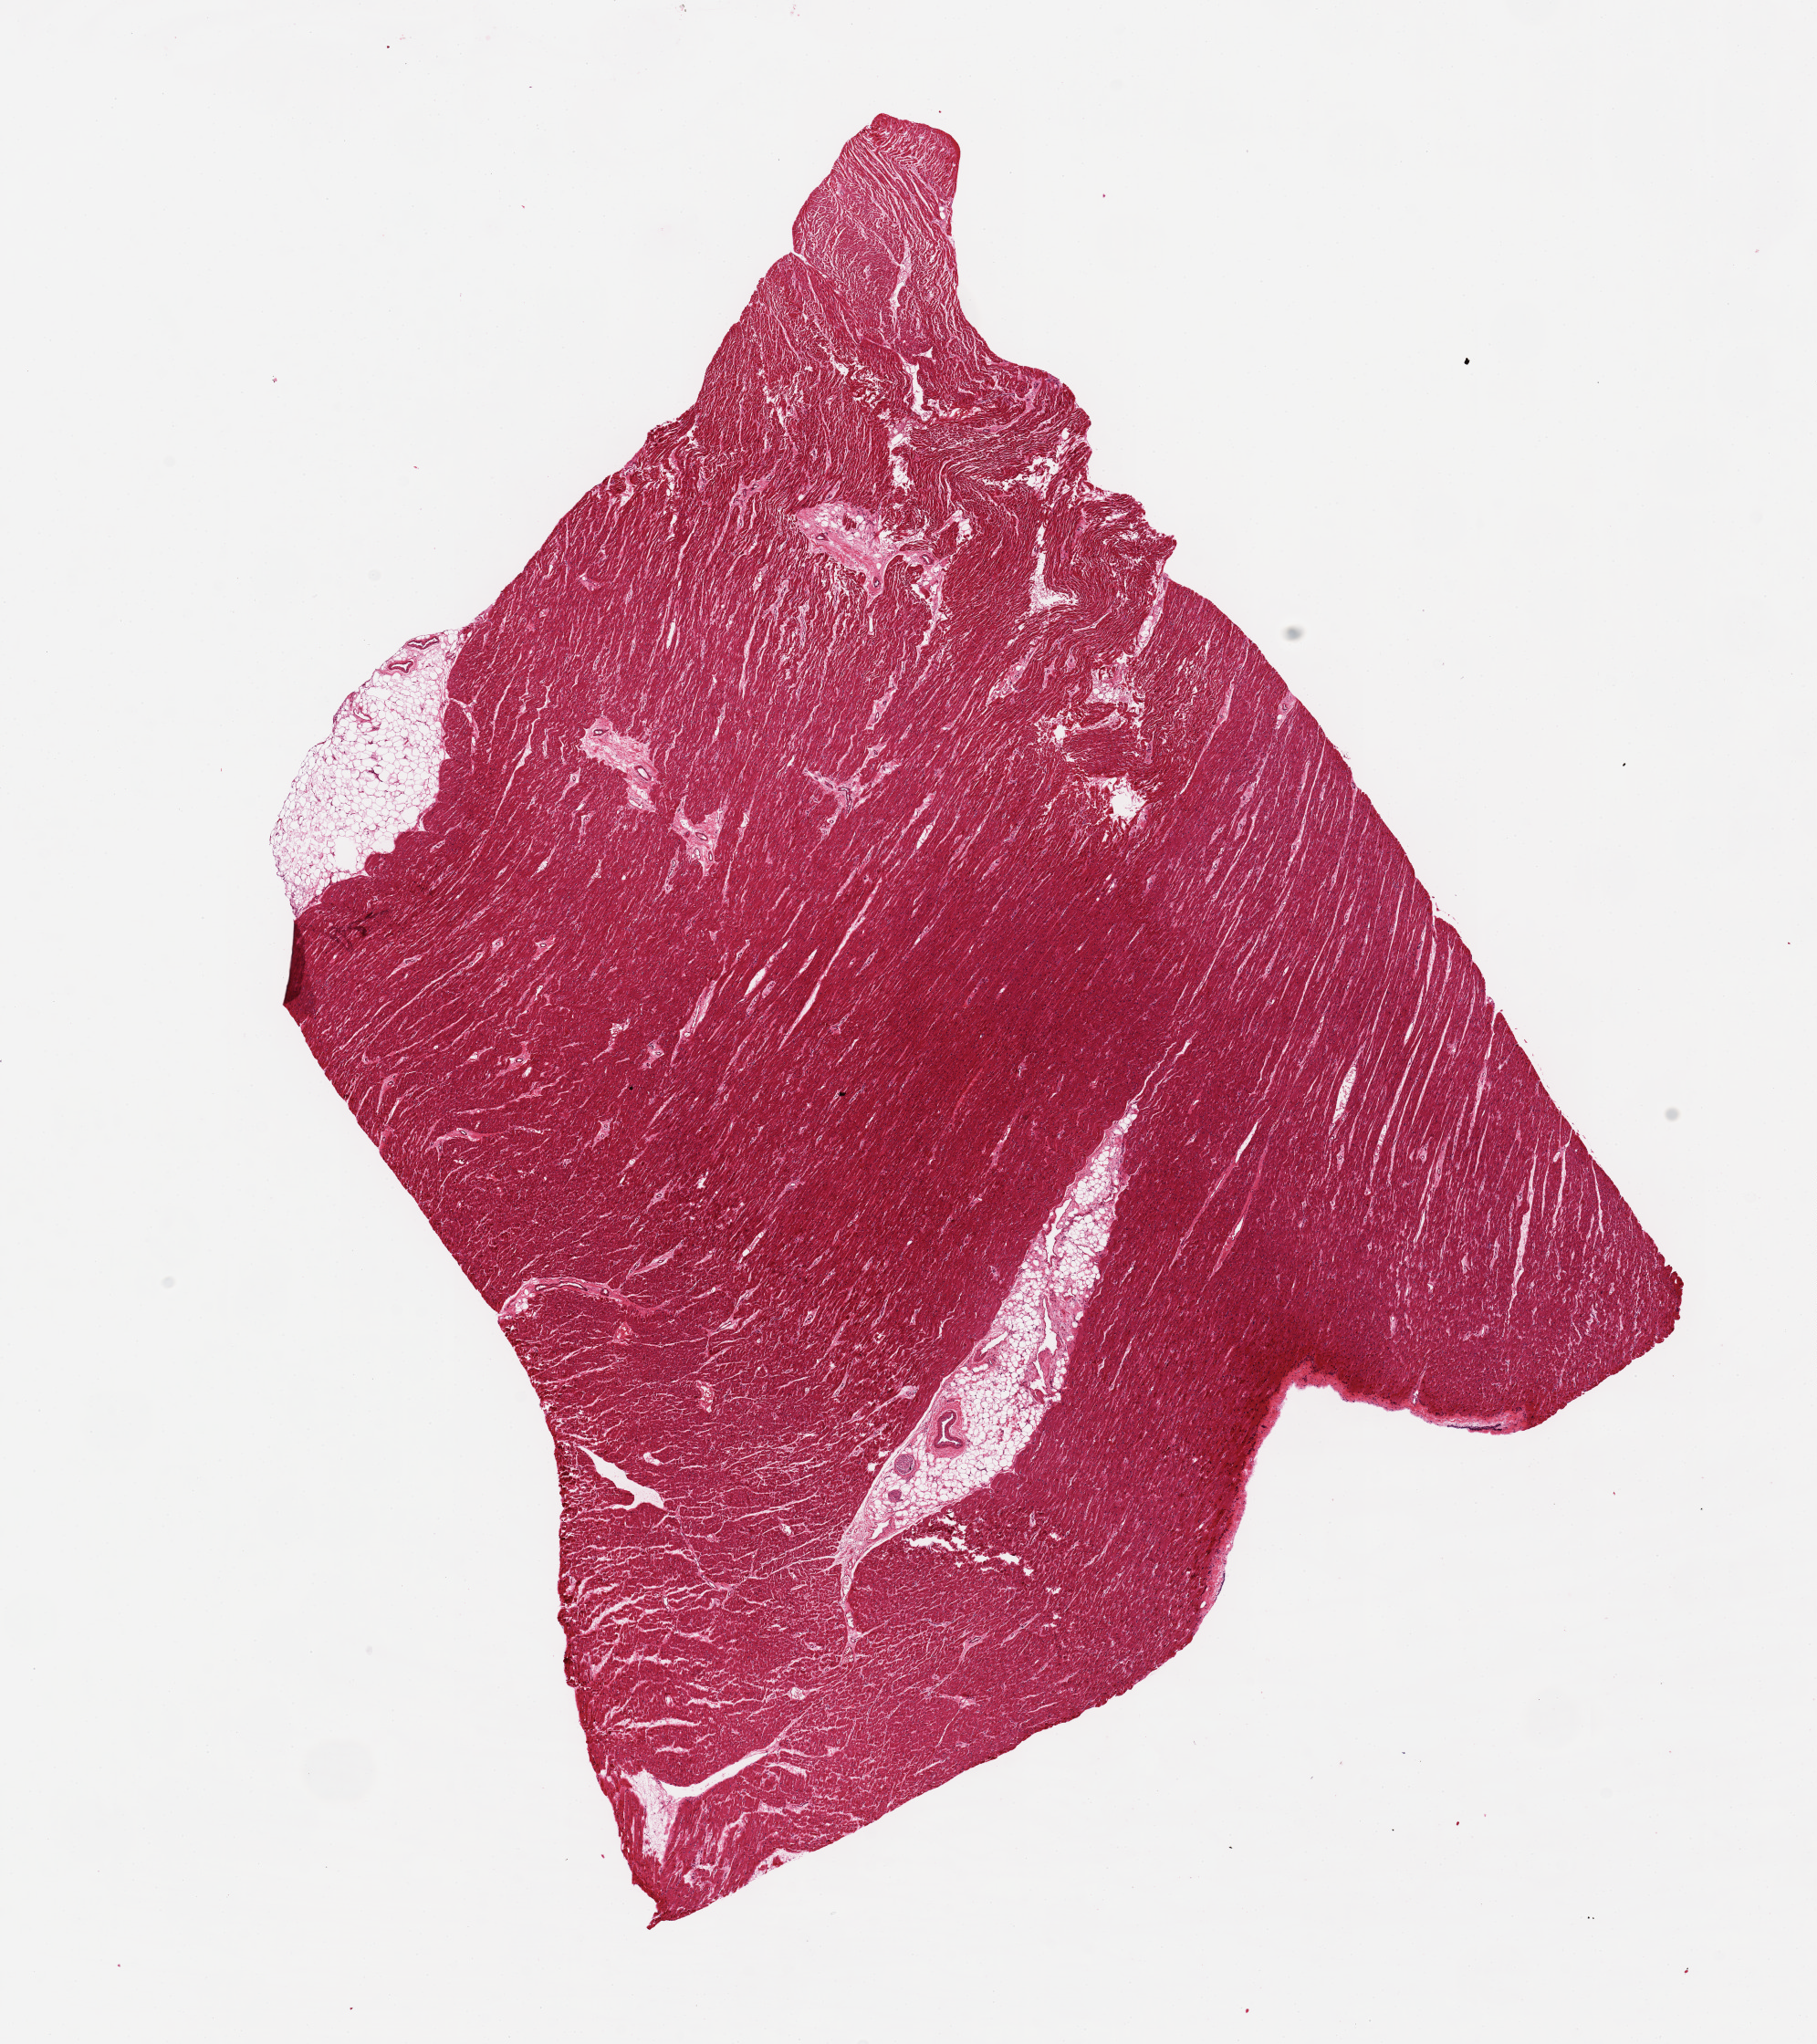
Whole-slide image, H&E stain — a low-resolution overview of the entire scanned area, about 15.8 x 17.7 mm, PAXgene-fixed paraffin-embedded (PFPE) section, section of heart (target tissue), donor tissue sample. Male donor.
Reviewer comment on this tissue sample: Incorrect specimen???12.5x15.5 mm cardiac muscle, autolysis score 1.Central areas (fat) with poor fixation.